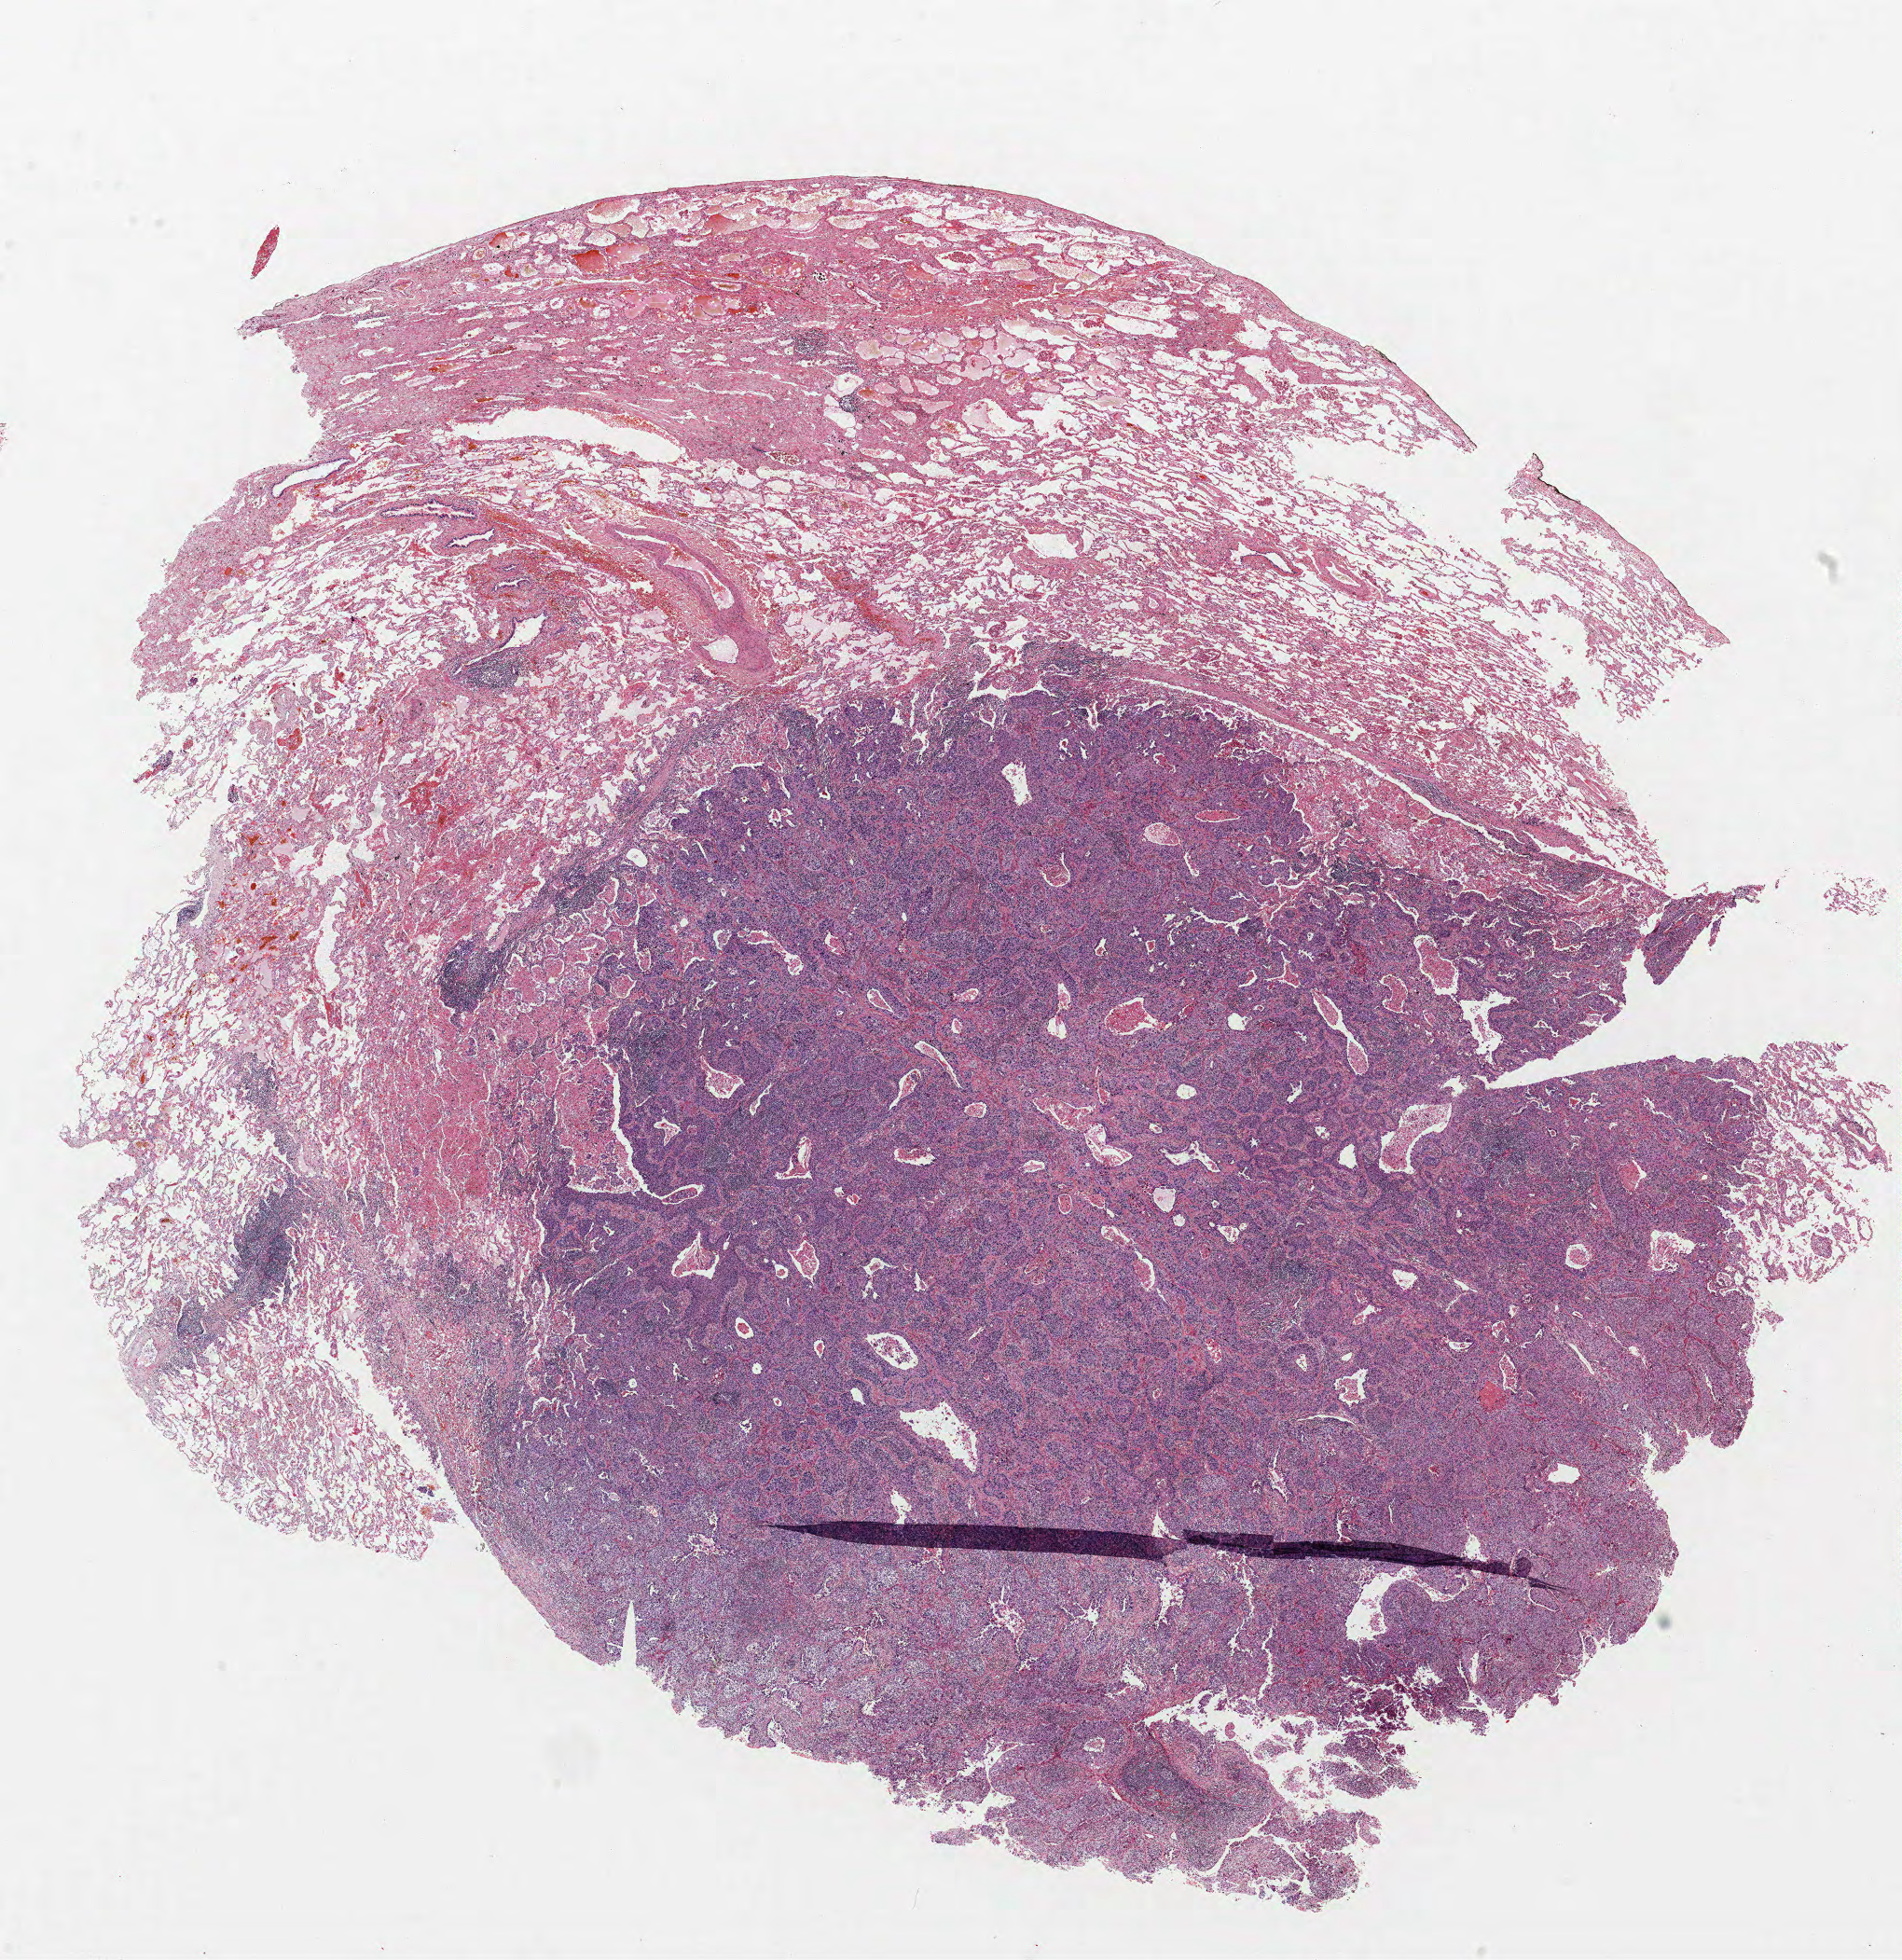
Hematoxylin and eosin (H&E) stained whole-slide image — a low-resolution overview of the entire scanned area, about 16.3 x 16.8 mm (acquisition: 40x scan); FFPE section; lung tissue. Female patient, aged 56 at enrolment. Former smoker at enrolment. Grade: poorly differentiated (G3).
Primary tumour location (clinical record): right upper lobe. Tumour size (pathology): 11 mm. Stage (AJCC 6th edition): IA. Participant's lung-cancer diagnosis: Squamous cell carcinoma, NOS.